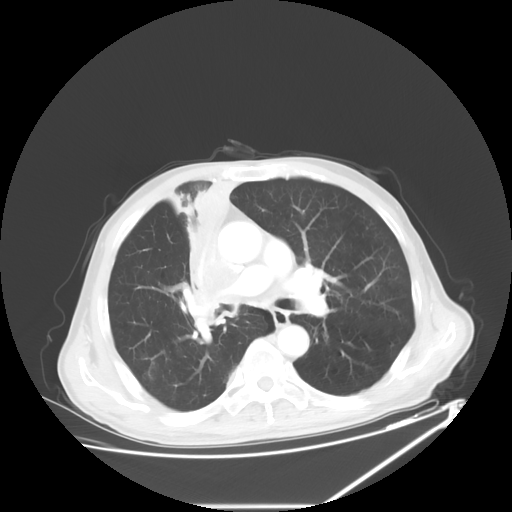
Chest CT, one axial slice. Lung window (W 1500 / L -600 HU). 5 mm slice thickness. 512 × 512 image matrix. Male patient, age 73 years. Case-level facts recorded for this patient, not image findings: clinical TNM (as recorded): T2a N1 M0.
Outlined on this slice (rectangle marked by the reading radiologist):
- lung tumour (recorded histology: squamous cell carcinoma): bounding box (x1, y1, x2, y2) in pixels: (176, 164, 241, 333)